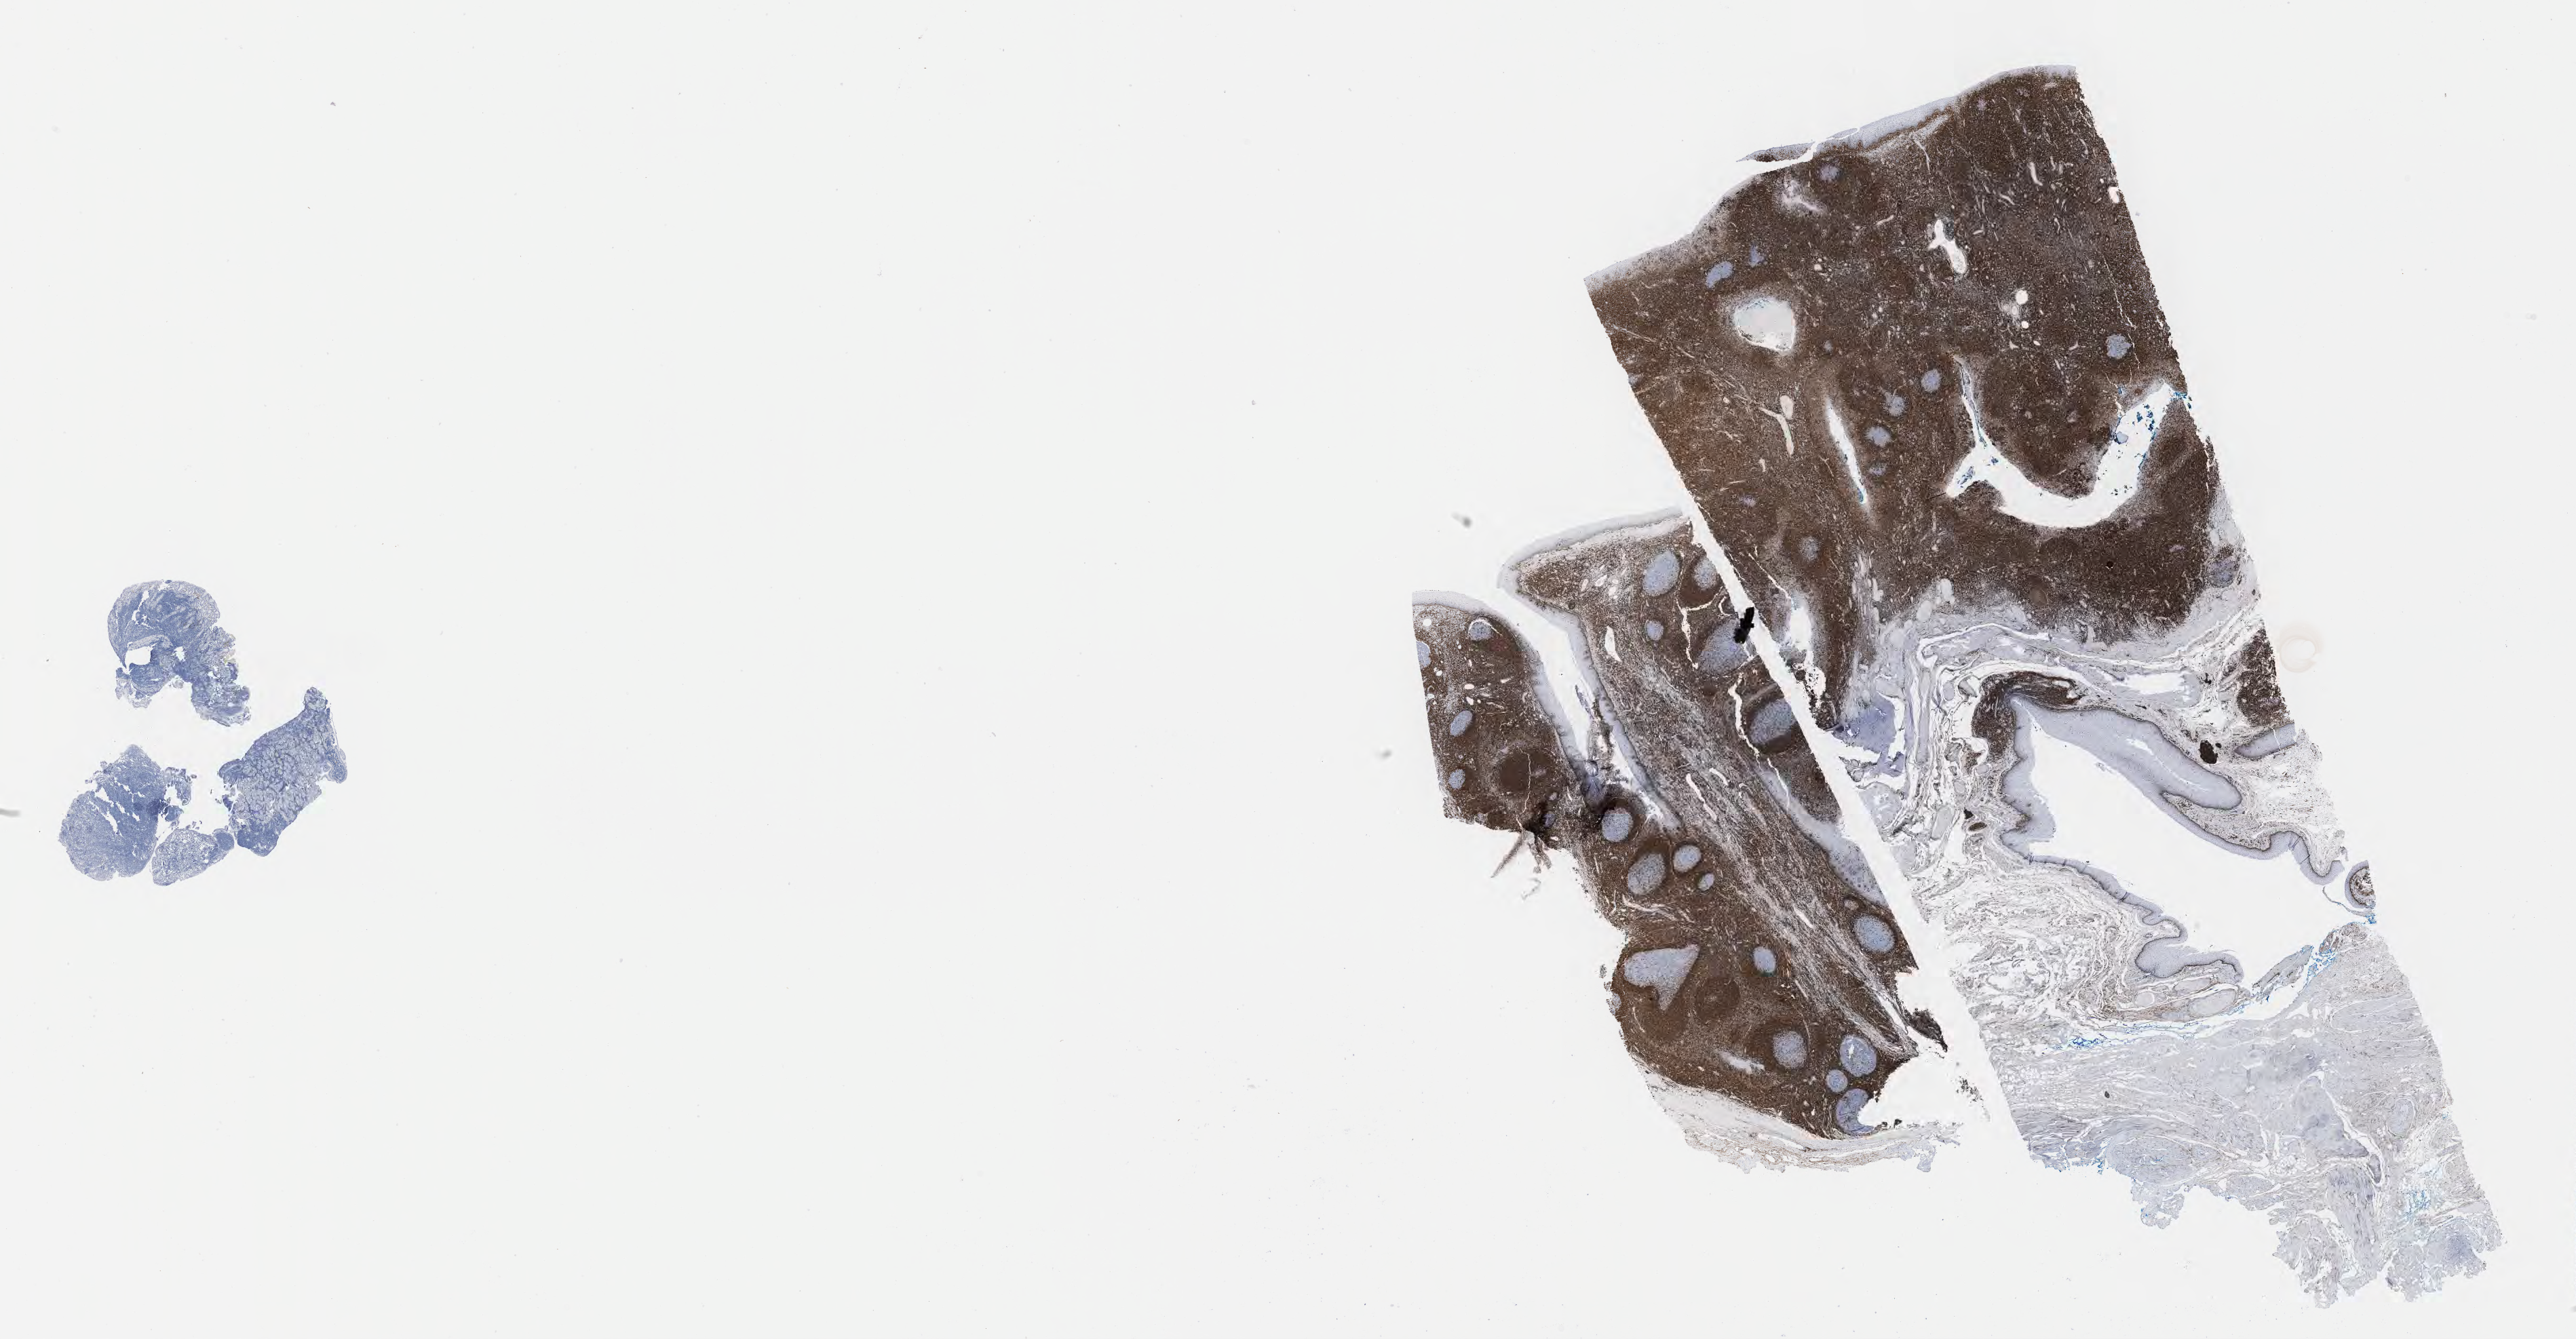
IHC for BCL2, whole-slide image — a low-resolution overview of the entire scanned area, about 30.7 x 16.0 mm; specimen: tumor tissue. Patient: female, aged 45.
Diagnosis: Burkitt lymphoma, NOS.